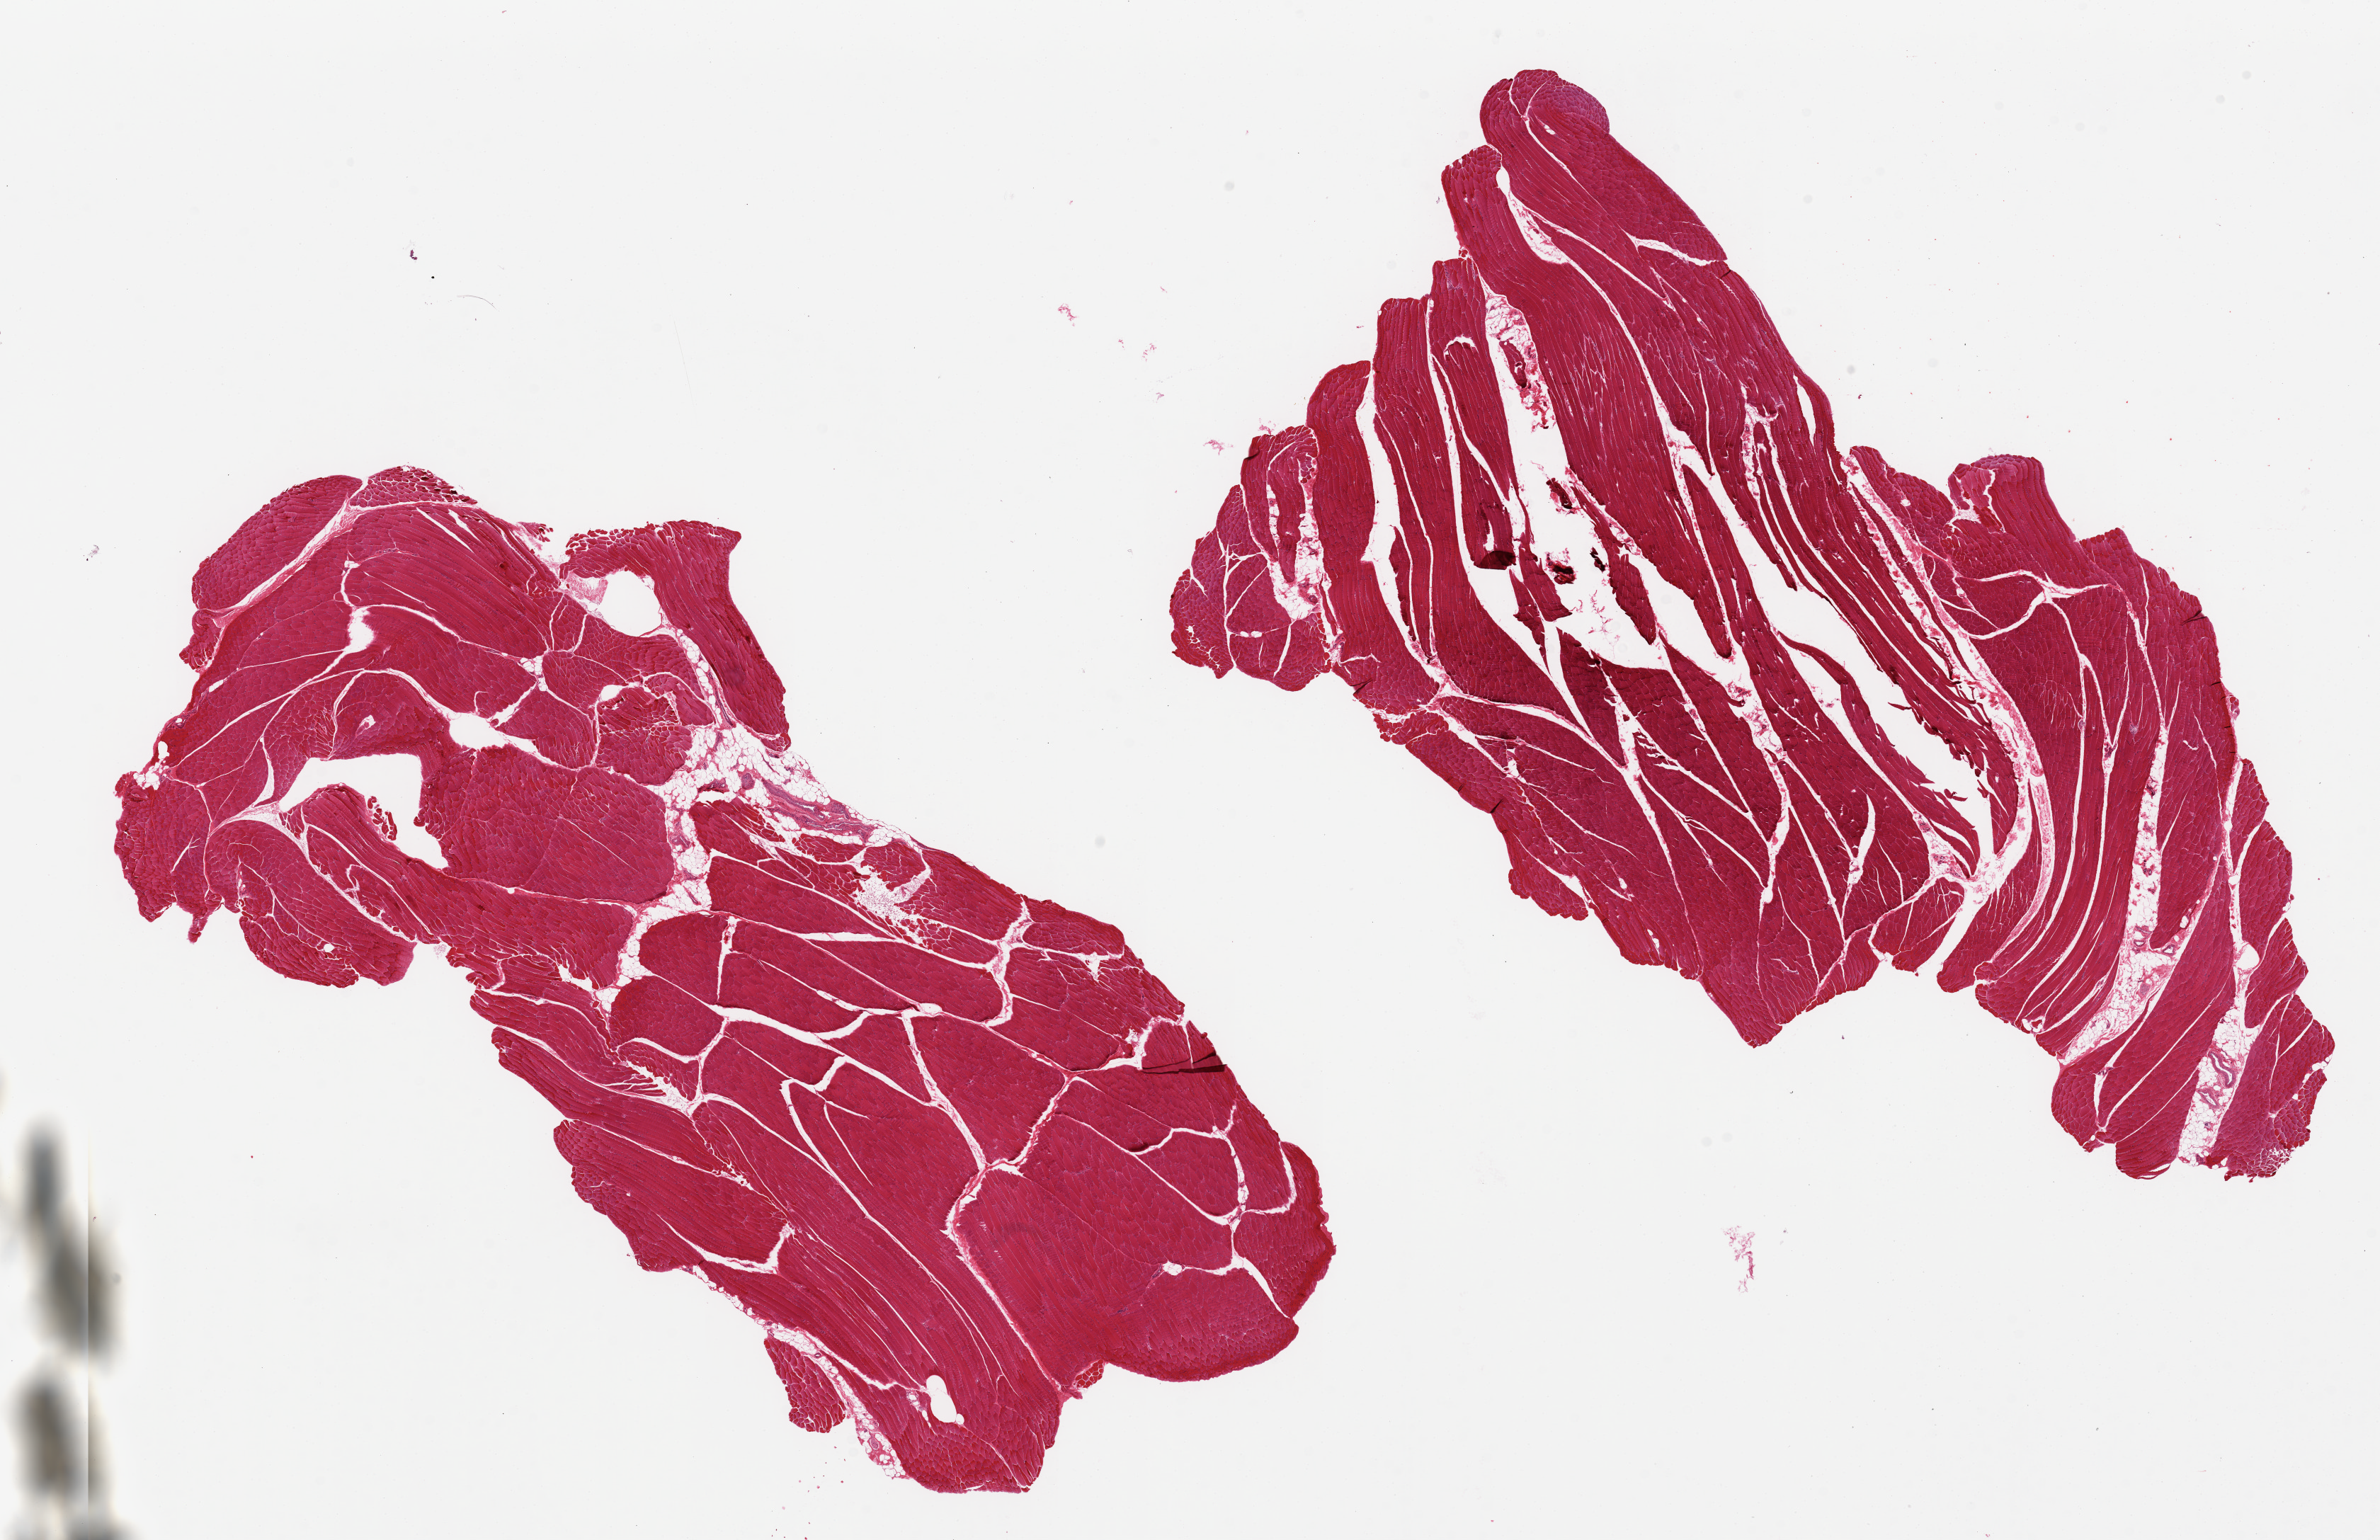
Digitized haematoxylin and eosin-stained section, shown as a low-resolution overview of the whole scanned area (about 26.6 x 17.2 mm, from a 20x scan). PAXgene-fixed, paraffin-embedded tissue. Section of skeletal muscle (target tissue). Donor tissue sample. Donor: male.
Review note (as recorded): 2 pieces, oversized, larger piece not fully intact (? poor fixation) and may include additional internal fat up to 10%, small attachment of tendon.